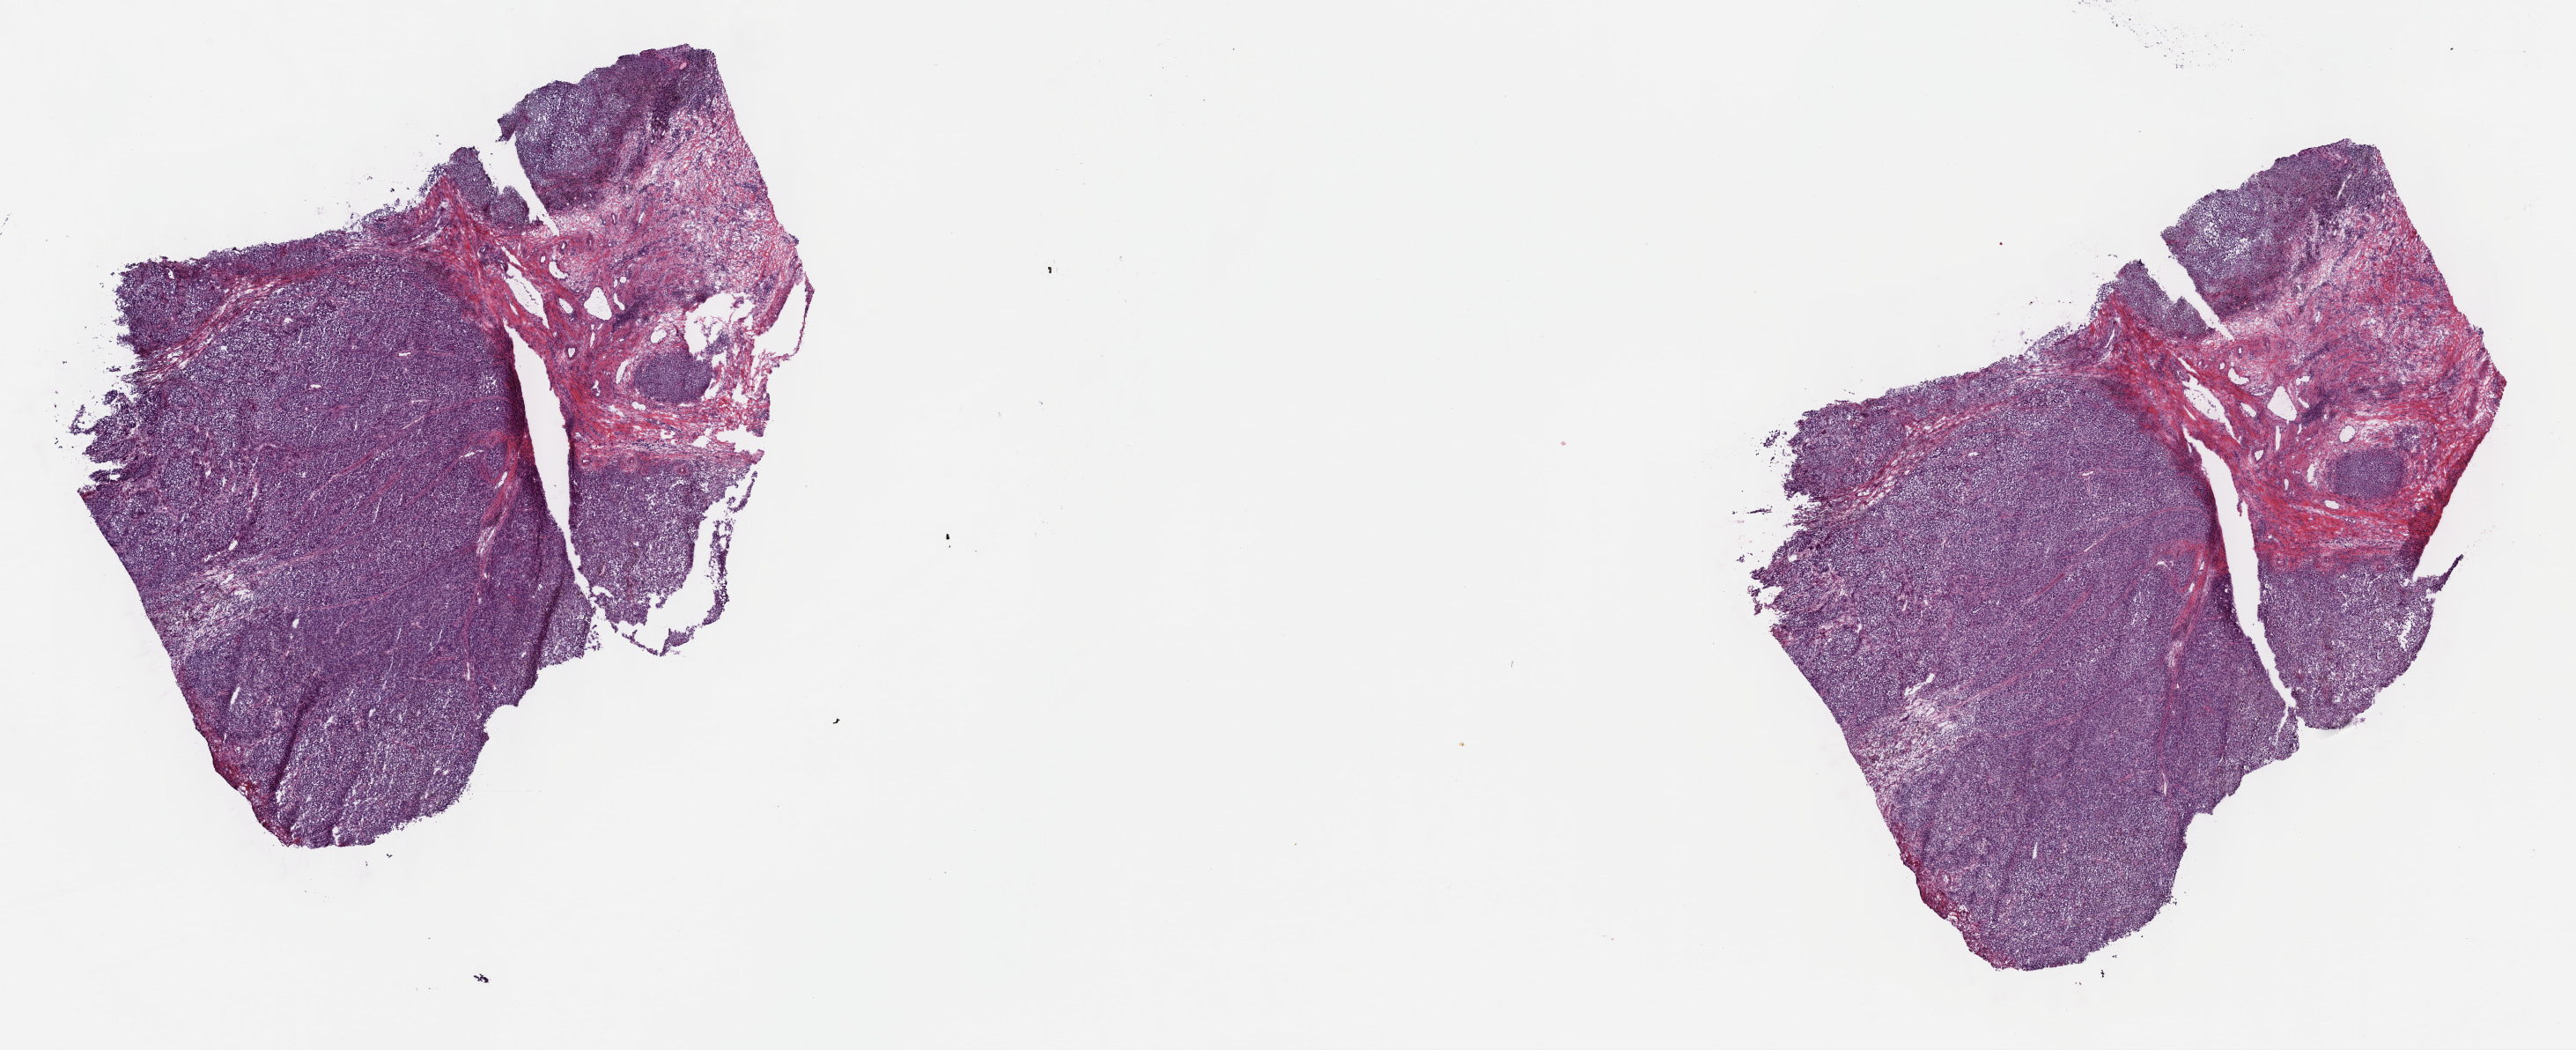
Digitized Hematoxylin and eosin (H&E) stained tissue section (whole slide) — a low-resolution overview of the entire scanned area, about 23.7 x 9.6 mm (slide scanned at 40x), frozen section, primary tumour sample from the skin. Male, age 61 years at initial diagnosis. Slide review estimates, as recorded: tumour cells 100%, tumour nuclei 75%, normal cells 0%, stromal cells 0%, necrosis 0%. Infiltration values recorded for this section: lymphocyte infiltration 3%, monocyte infiltration 0%, neutrophil infiltration 0%.
Pathologic diagnosis: Epithelioid cell melanoma. AJCC pathologic stage: IIC (7th edition). TNM: T4b N0 M0.